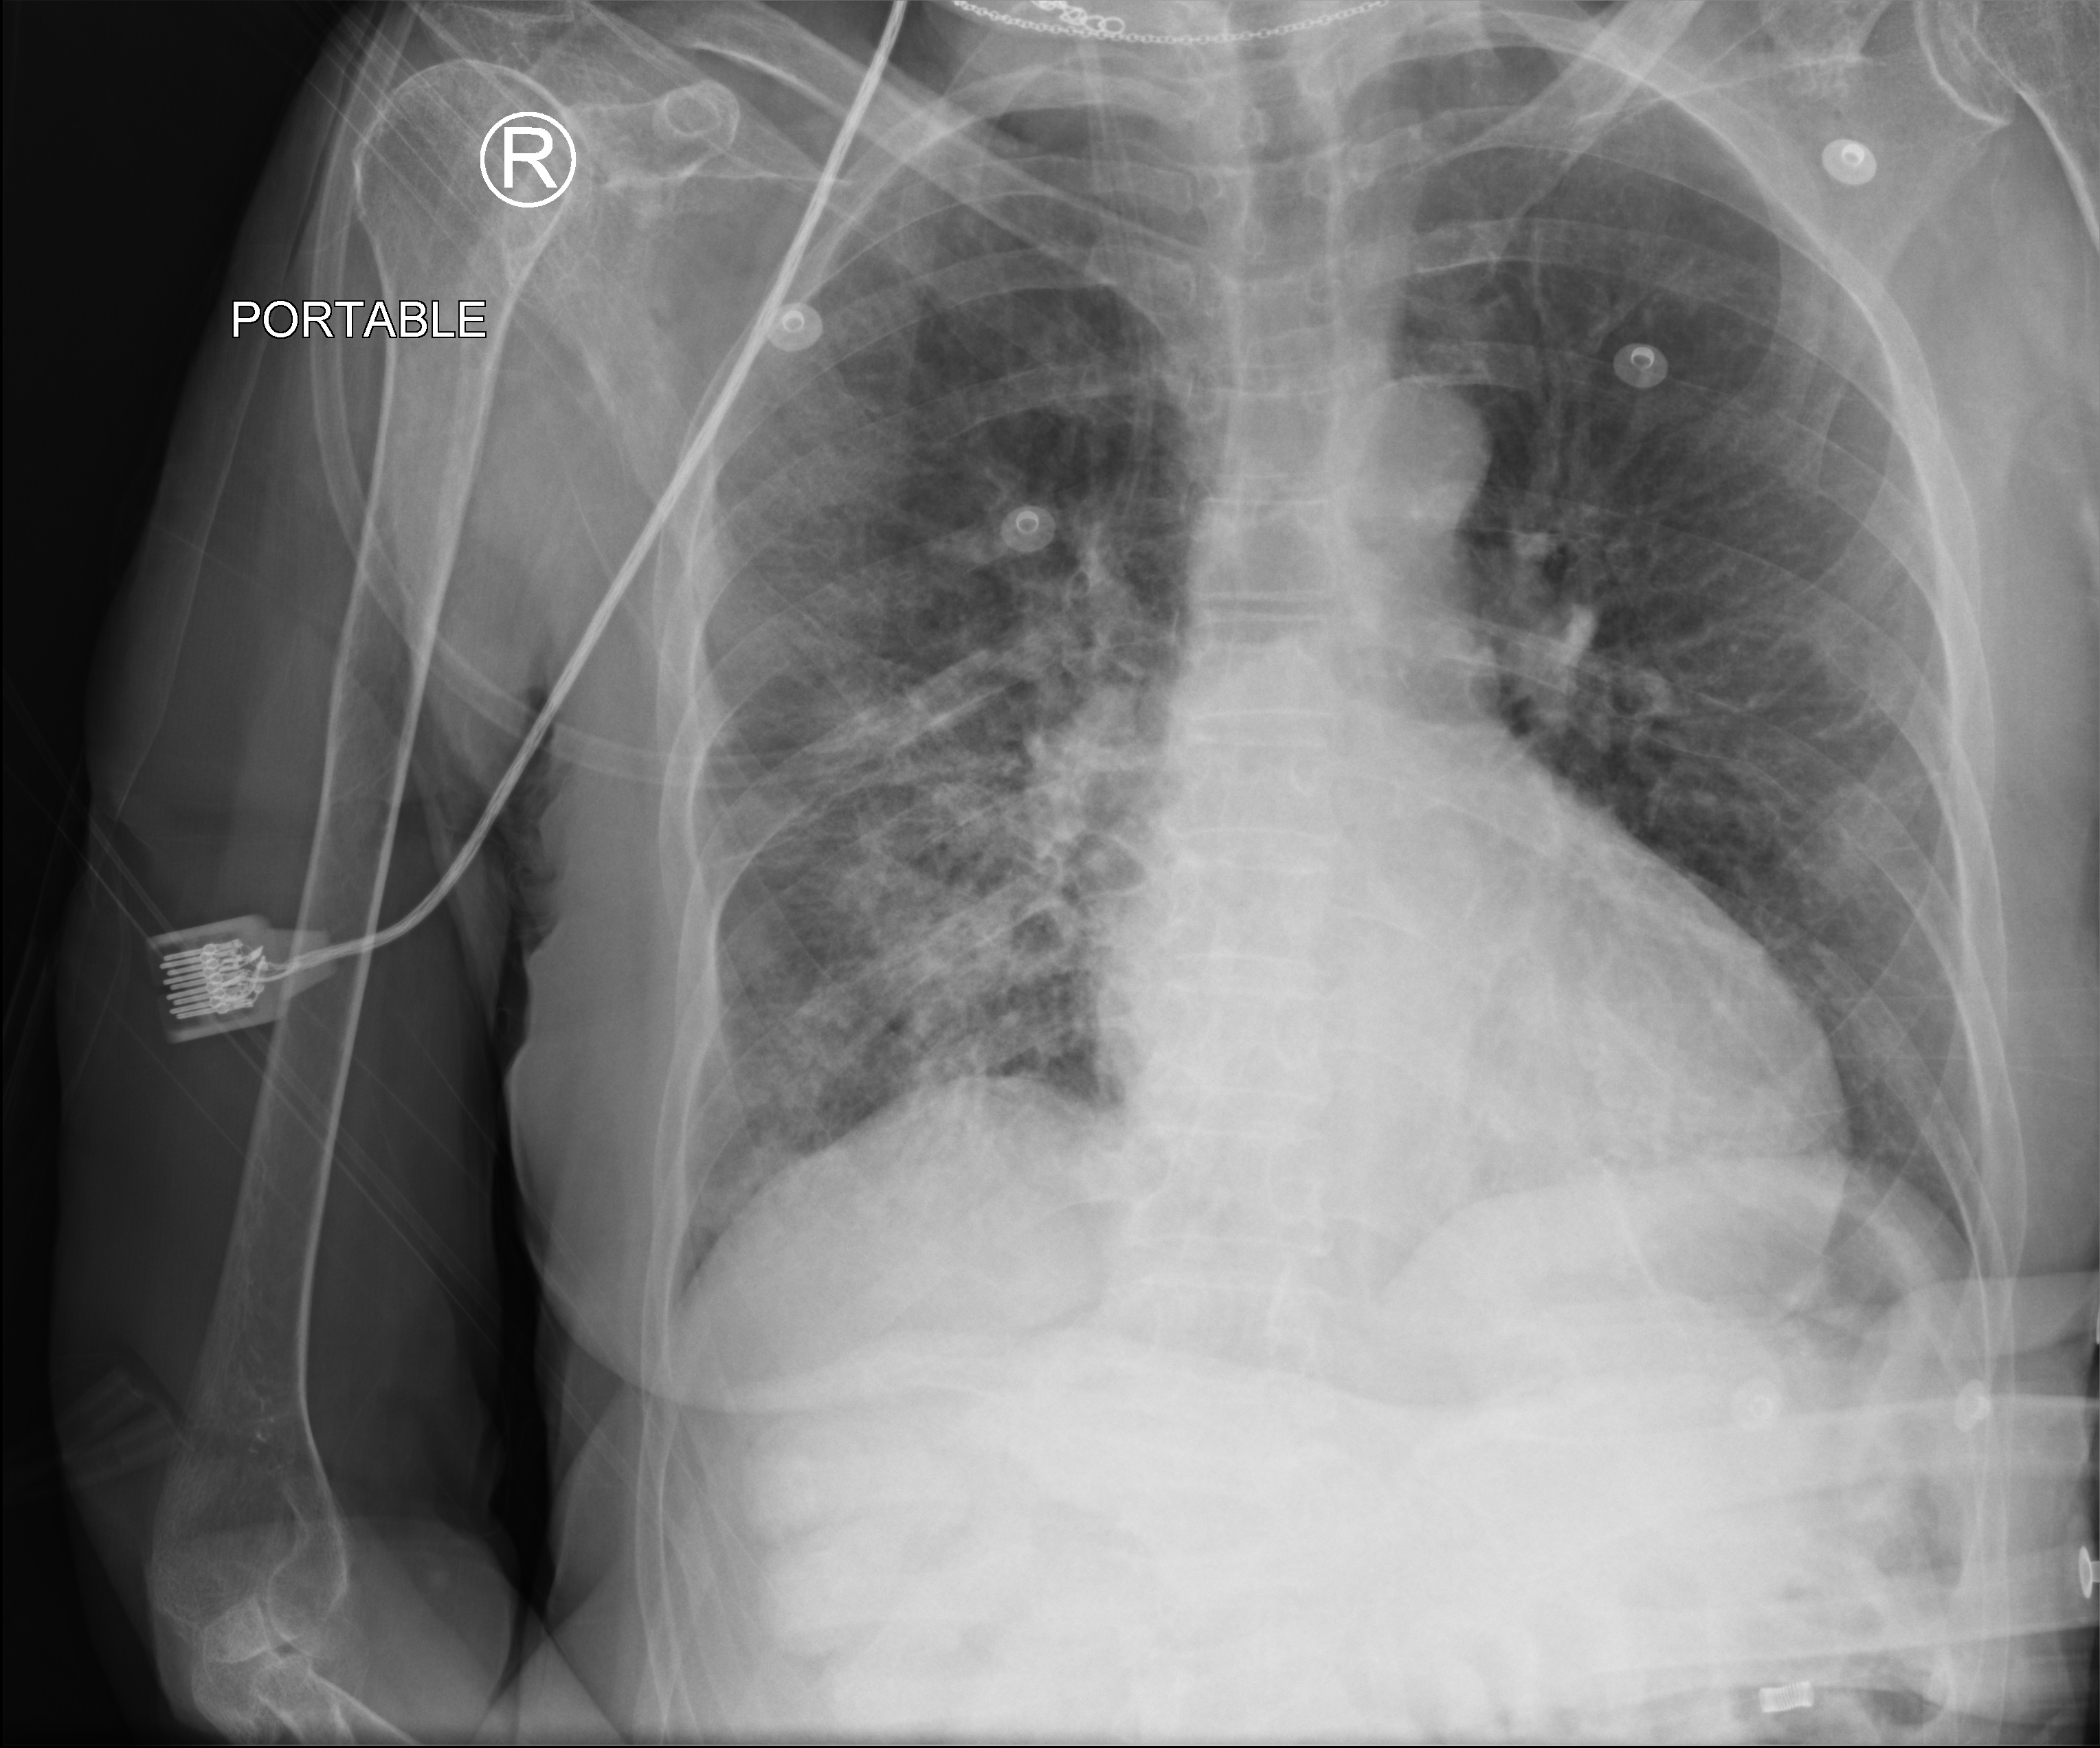
Portable chest radiograph; anteroposterior (AP) projection. Patient hospitalised with COVID-19; female, aged 75–90 years.
Hospital-stay facts (about this admission, not read from this image; timing relative to this image not recorded): diabetes (admission record): no; COPD (admission record): no.